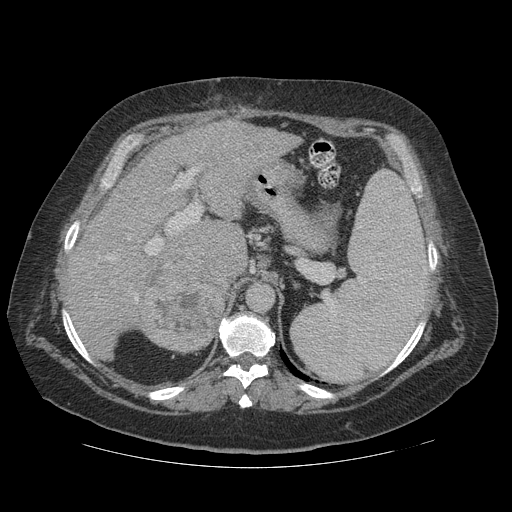
Contrast-enhanced abdominal CT (liver protocol), one axial slice; slice 79 of 121 in the series (ordered by position); 140 kVp; soft-tissue window (W 400 / L 40 HU); 2.5 mm slice thickness; 512 × 512 image matrix, field of view 420 × 420 mm. From the clinical record (not read from this slice): diagnosis: hepatocellular carcinoma (patient treated with transarterial chemoembolisation; whether this scan precedes or follows treatment is not stated here); TNM stage (as recorded): Stage-IIIA; Child-Pugh class: A; tumour differentiation: well differentiated; tumour nodularity: multinodular.
Outlined on this slice (semi-automatic segmentation, software-assisted and operator-edited):
- liver parenchyma outside the tumour (the mass and vessels are separate outlines, so this box may not span the whole liver): bounding box [x1, y1, x2, y2] px = [66, 120, 300, 354]
- mass: [132, 245, 231, 352]
- liver vessels: [94, 135, 235, 301]